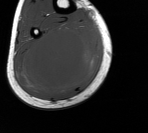
MRI of an extremity soft-tissue mass, one axial slice; position 57 of 76 along the scan axis; MR volume resampled by the dataset authors to the PET/CT grid (not the native acquisition matrix); 148 × 133 image matrix. Male patient. From the clinical record (not read from this slice): histological type: liposarcoma - round cell; grade: high; site of the primary tumour: right calf.
Outlined on this slice (expert contour drawn on MRI and transferred to this co-registered scan by the dataset authors):
- gross tumour volume (mass): bounding box (x1, y1, x2, y2) in pixels: (15, 19, 101, 97)